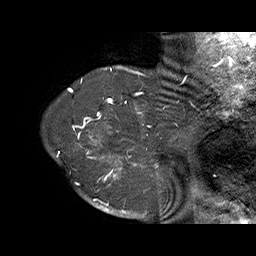
Breast MRI (dynamic contrast-enhanced), one sagittal slice. Position 60 of 70 along the scan axis. Dynamic contrast-enhanced series, time point 2 of 6 at this slice position (early post-contrast). 1.5 T. TE 4.5 ms, TR 32.4 ms. 3 mm slice thickness. 256 × 256 image matrix, field of view 180 × 180 mm. Female patient. Case-level facts recorded for this patient, not image findings: setting: breast cancer imaged before/during neoadjuvant chemotherapy; receptor status: HR-positive, HER2-negative.
Structures marked on this image (semi-automatically segmented with operator editing):
- analysis volume of interest (the breast-tissue region the enhancement analysis was run in; not a lesion): box from (x=71, y=128) to (x=159, y=202) px
- tumour enhancement mask (voxels above the 100 % enhancement threshold inside the analysis volume of interest): (x=73, y=128)–(x=158, y=202)